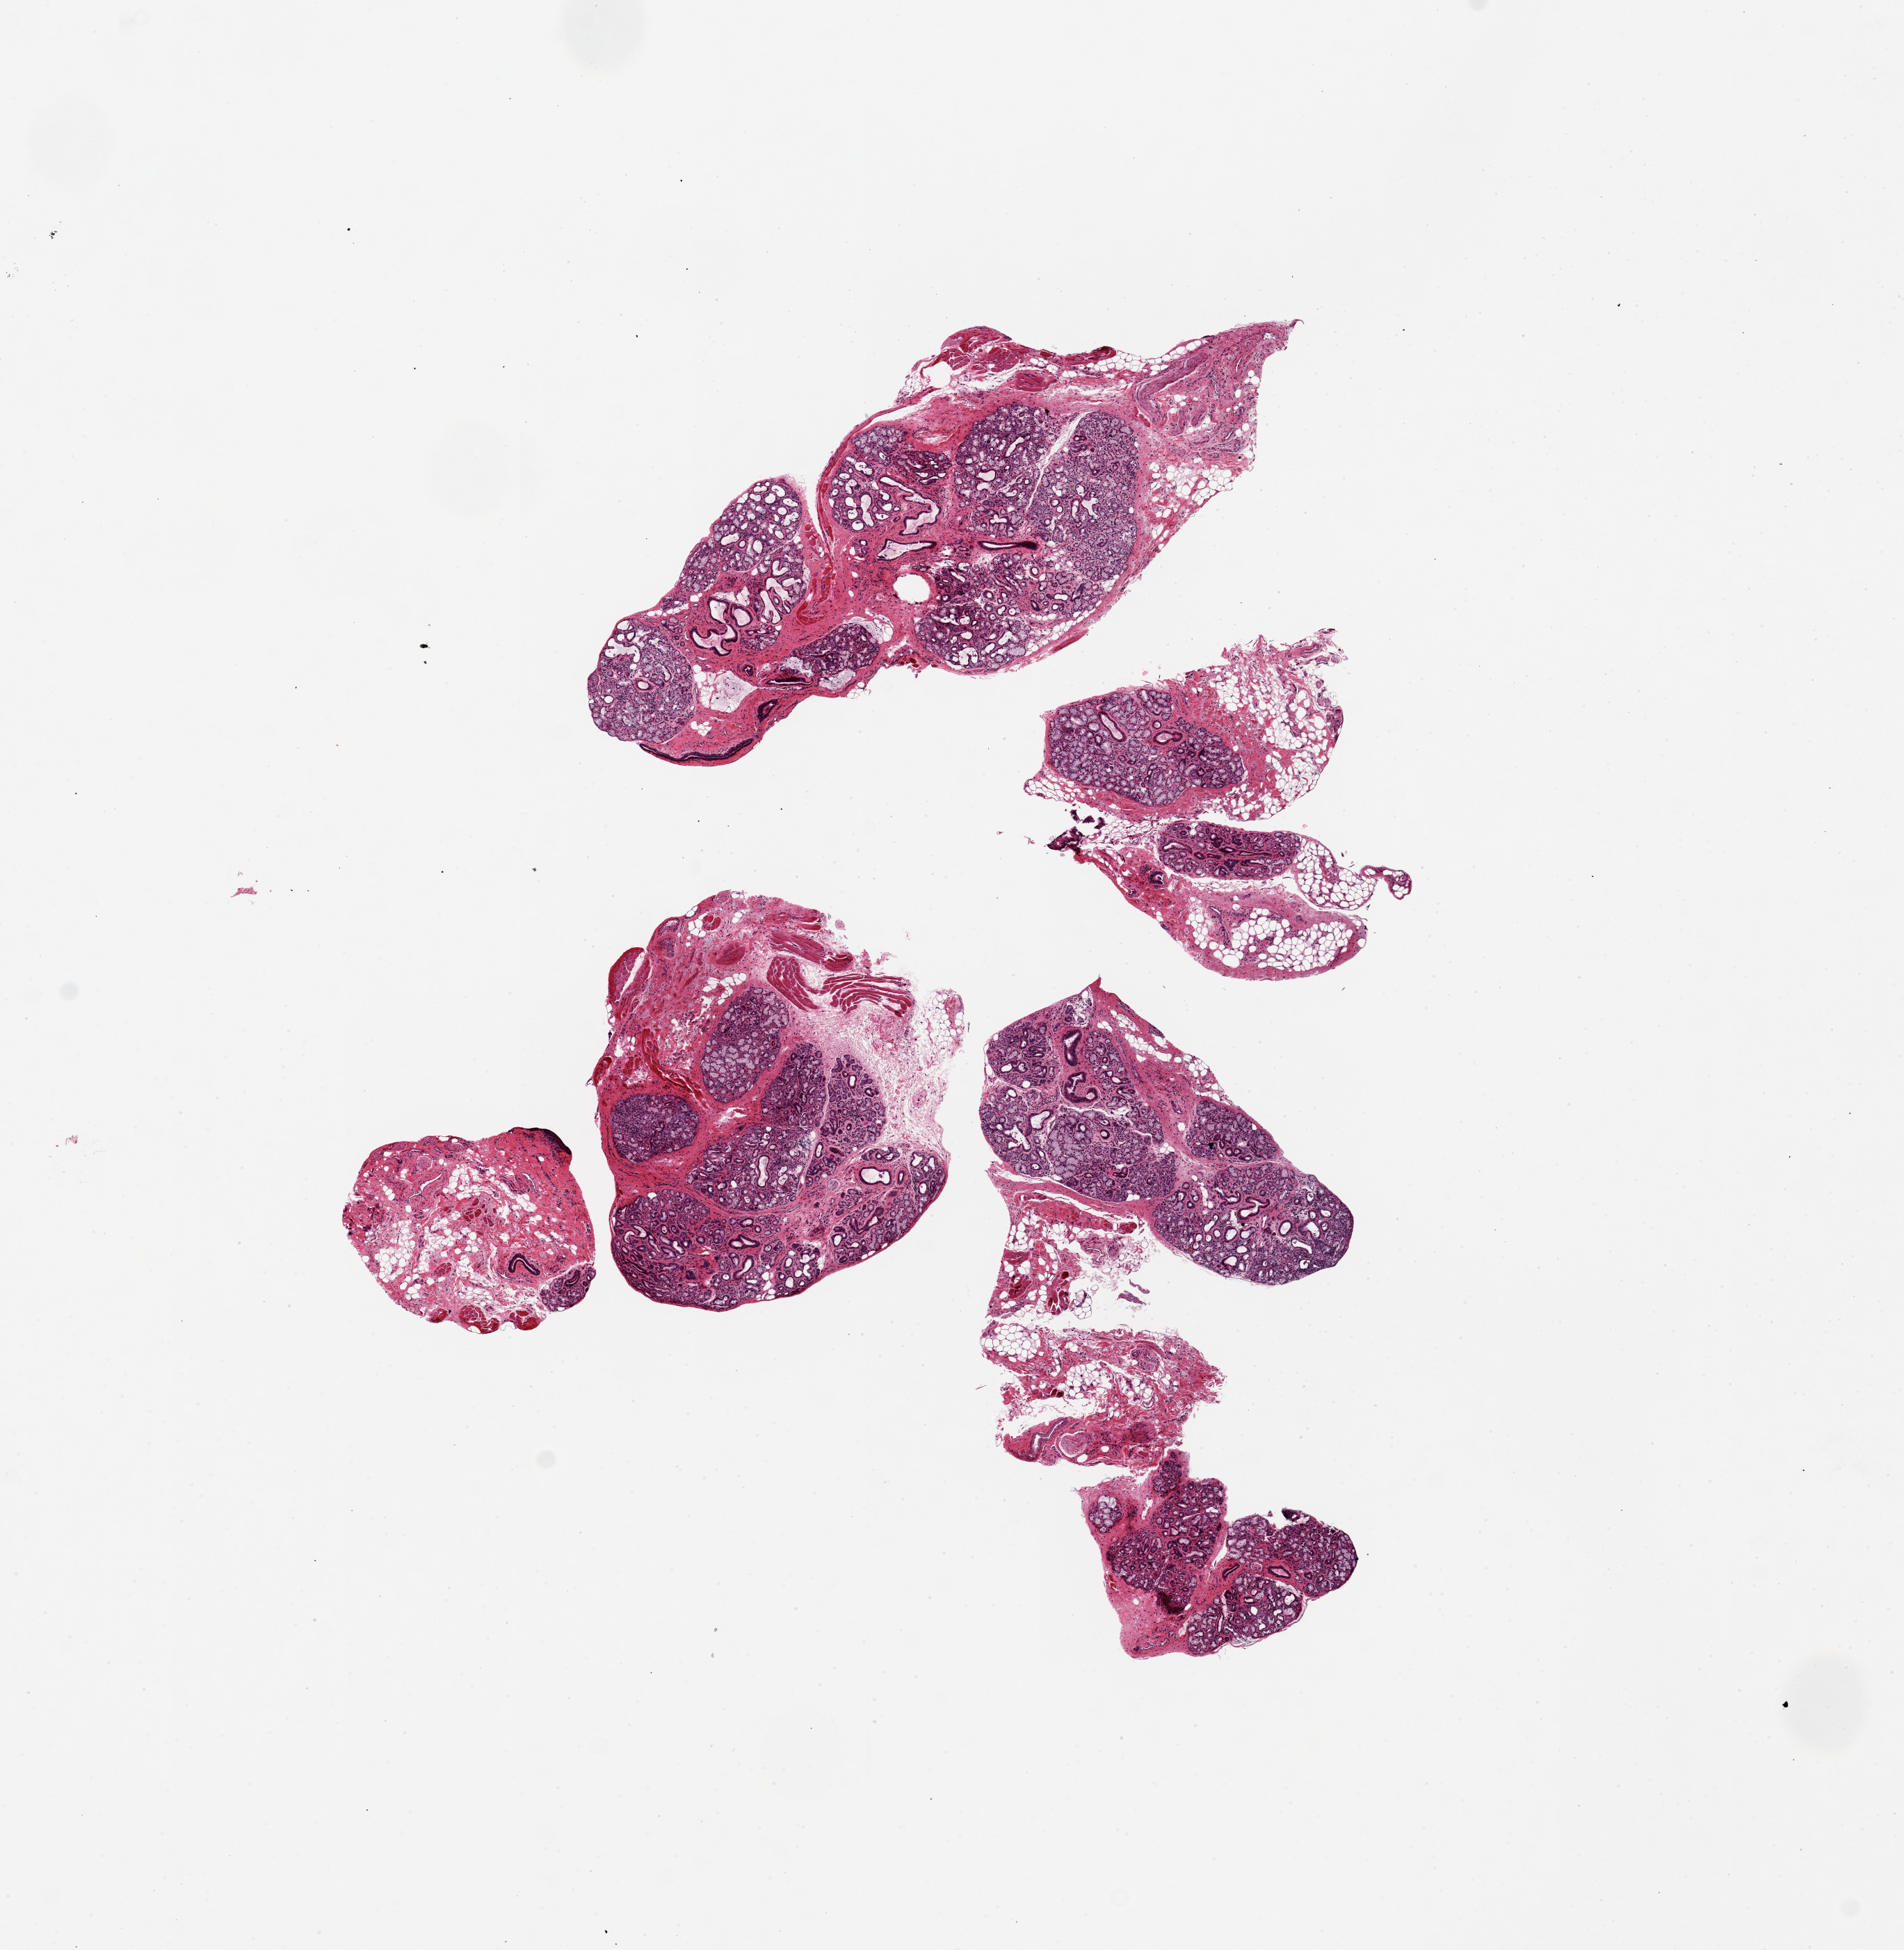
Hematoxylin and eosin (H&E) whole-slide image — whole scanned area (about 10.8 x 11.1 mm, slide scanned at 20x) shown as a low-resolution overview. PAXgene-fixed paraffin-embedded (PFPE) section. Target tissue: minor salivary gland. Tissue donor sample. Female donor.
Reviewer comment on this tissue sample: 4 pieces, up to 5x2mm; ~70% glandular tissue, well-preserved, rest is stroma.